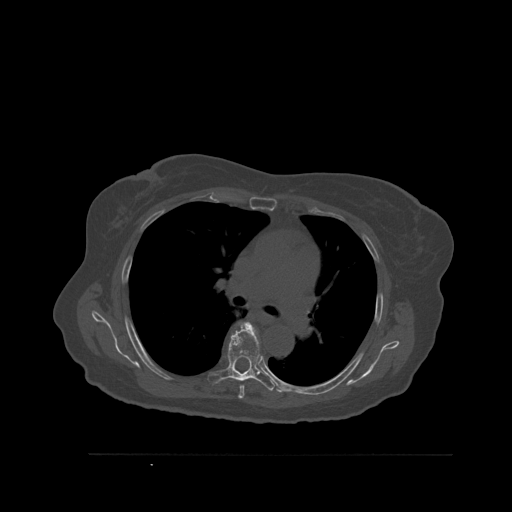
CT including the spine, one axial slice. Slice 384 of 527 in the series (ordered by position). Bone window (W 1800 / L 400 HU). 1.5 mm slice thickness. 512 × 512 image matrix, field of view 470 × 470 mm. Patient: female, 73 years. From the clinical record (not read from this slice): primary cancer: breast; vertebrae with lytic lesions (as recorded): L2.
Annotated regions visible in this slice (semi-automatic segmentation, software-assisted and operator-edited):
- T5 vertebra: bounding box (x1, y1, x2, y2) in pixels: (238, 385, 245, 399)
- T6 vertebra: (208, 322, 276, 391)